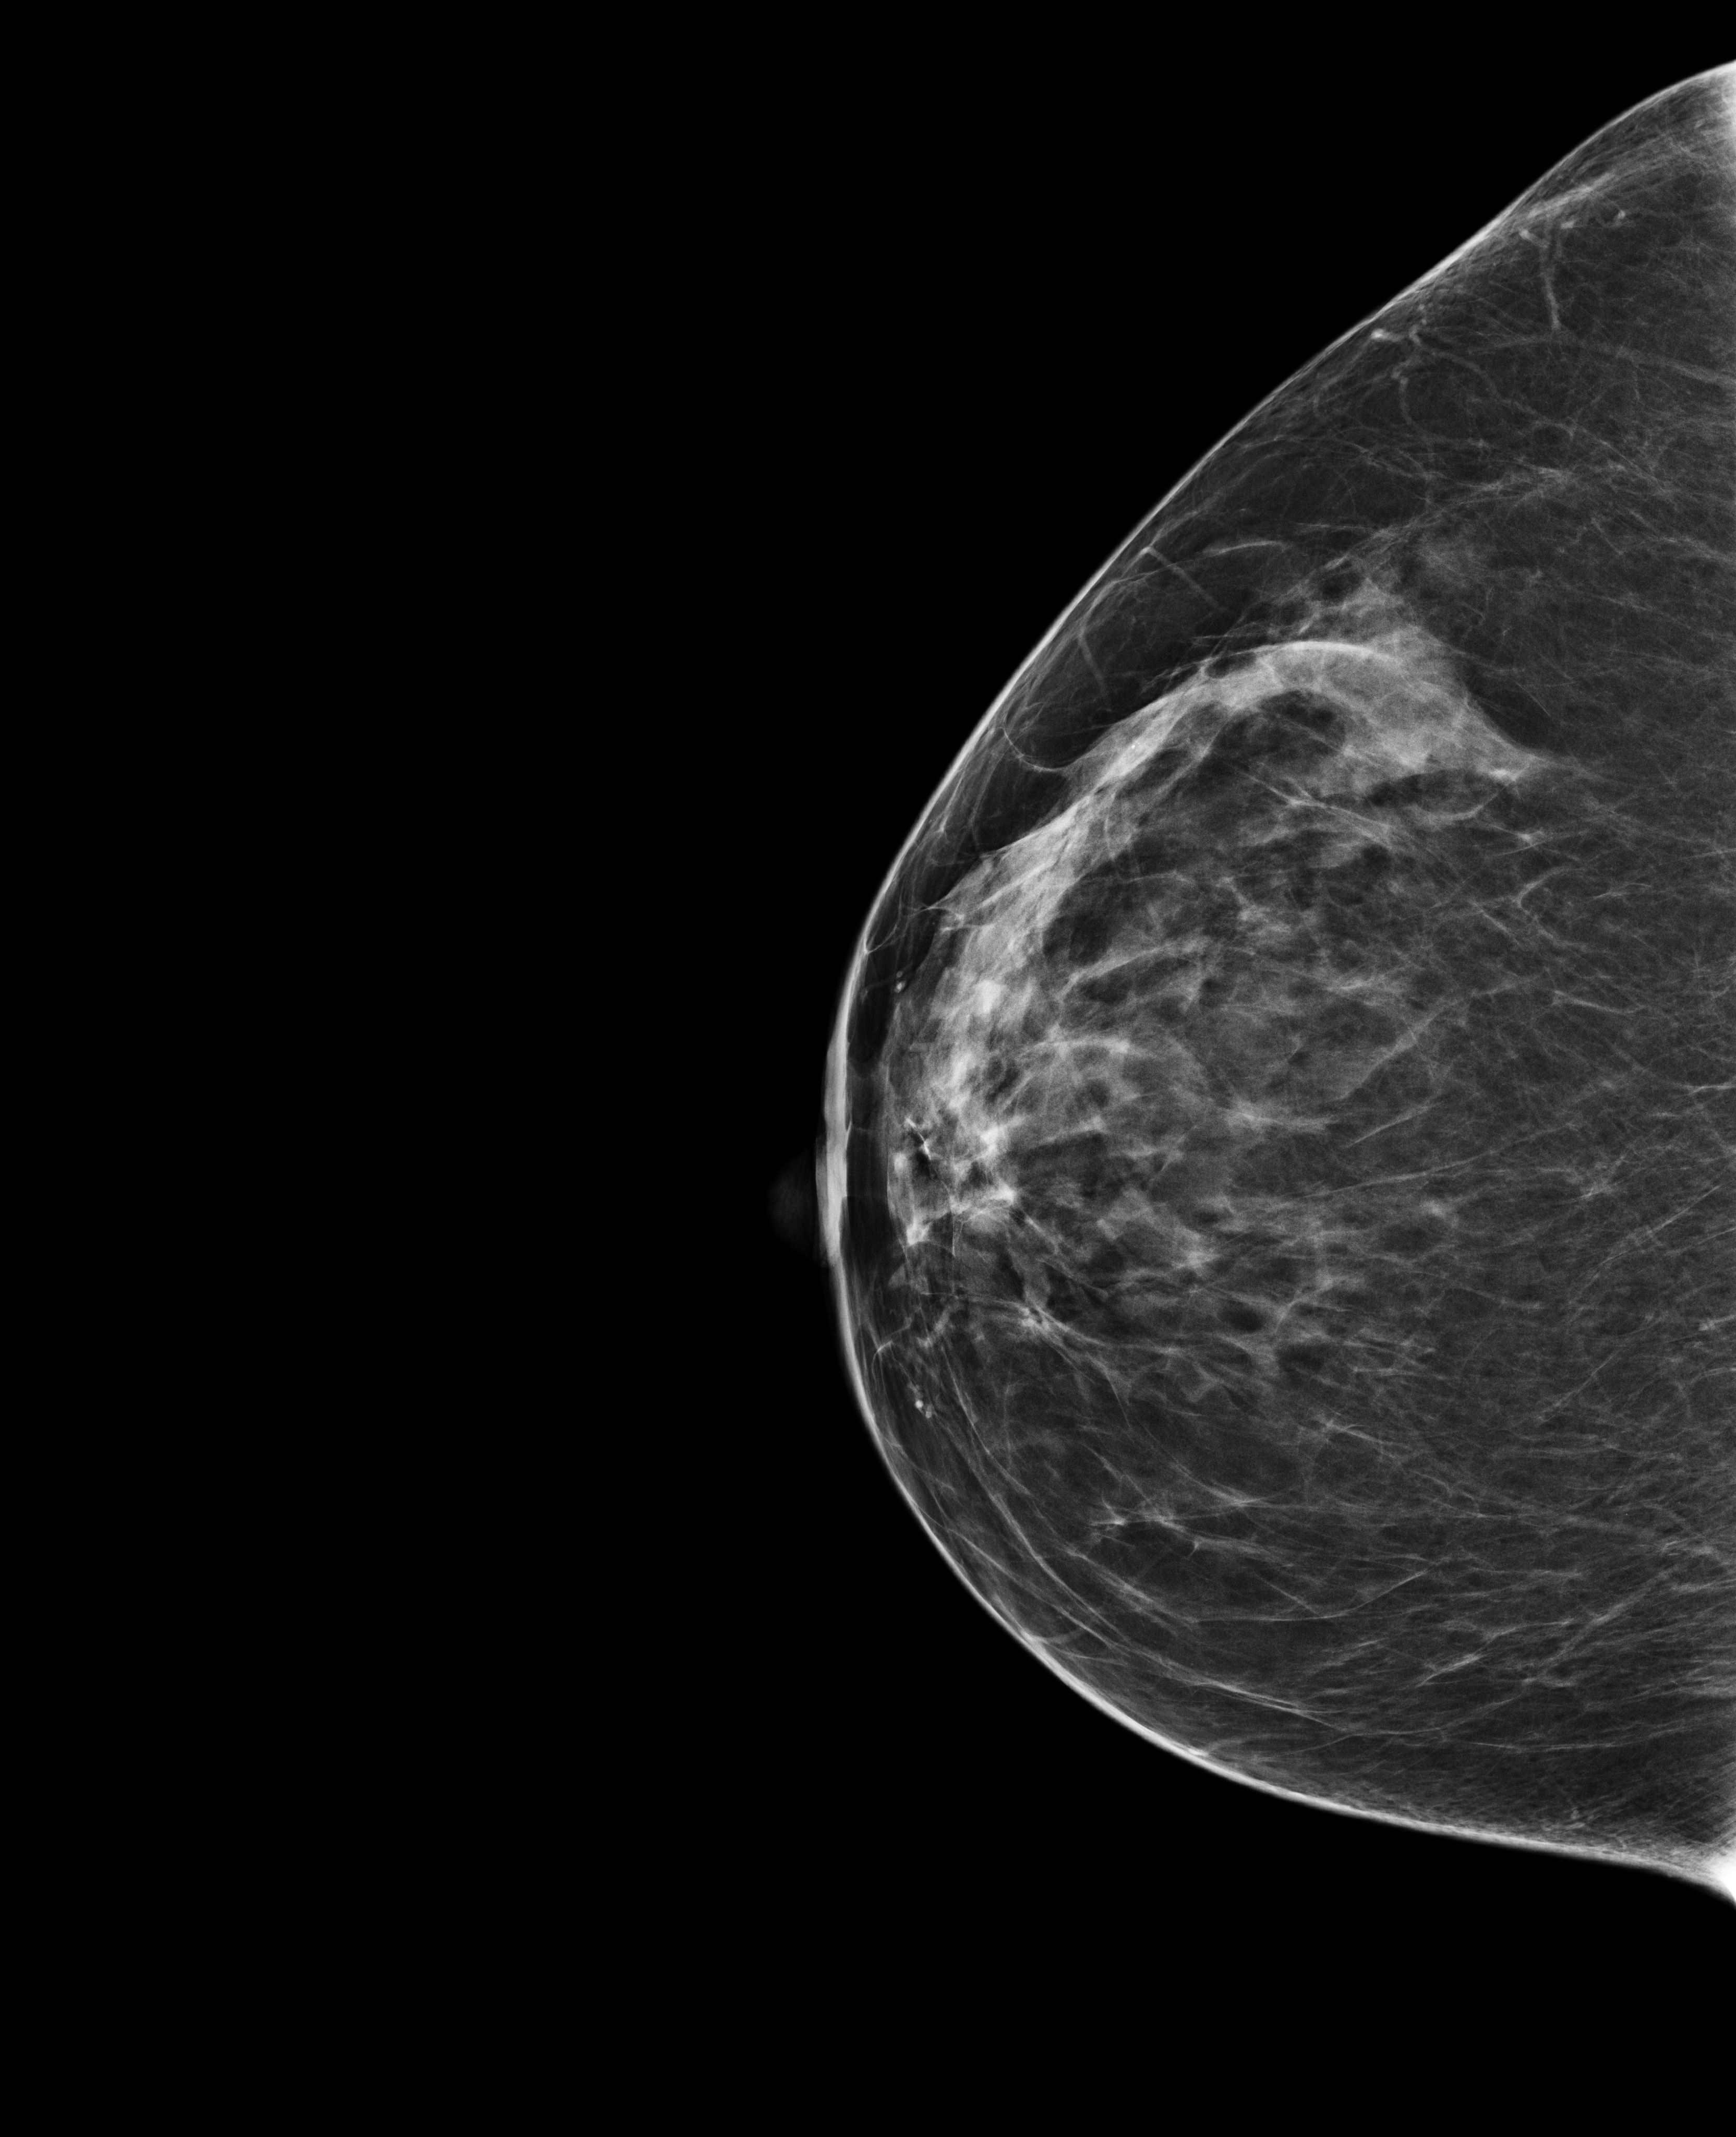
Annual screening mammography examination; compressed breast thickness 77 mm. Female patient, age 58 years.
Image type: full-field digital mammogram. Breast: right. Projection: craniocaudal (CC) view.